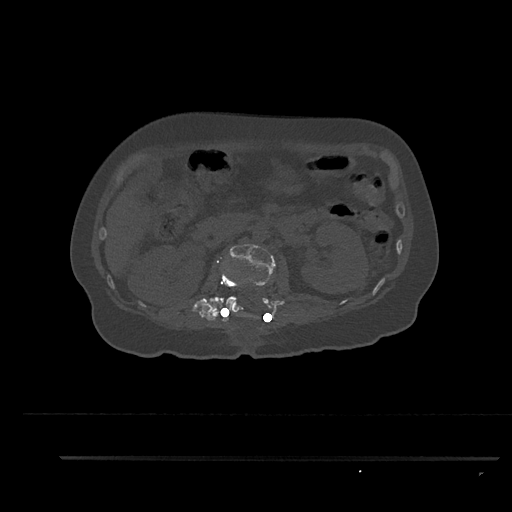
CT including the spine, one axial slice; position 188 of 797 along the scan axis; reconstruction kernel Br40s/3; bone window (W 1800 / L 400 HU); 0.5 mm slice thickness; 512 × 512 image matrix, field of view 408 × 408 mm. Female patient, age 44 years. From the clinical record (not read from this slice): primary cancer: renal.
Annotated regions visible in this slice (semi-automatically segmented with operator editing):
- L1 vertebra: bounding box [x1, y1, x2, y2] px = [221, 265, 242, 317]
- L2 vertebra: [224, 244, 274, 318]